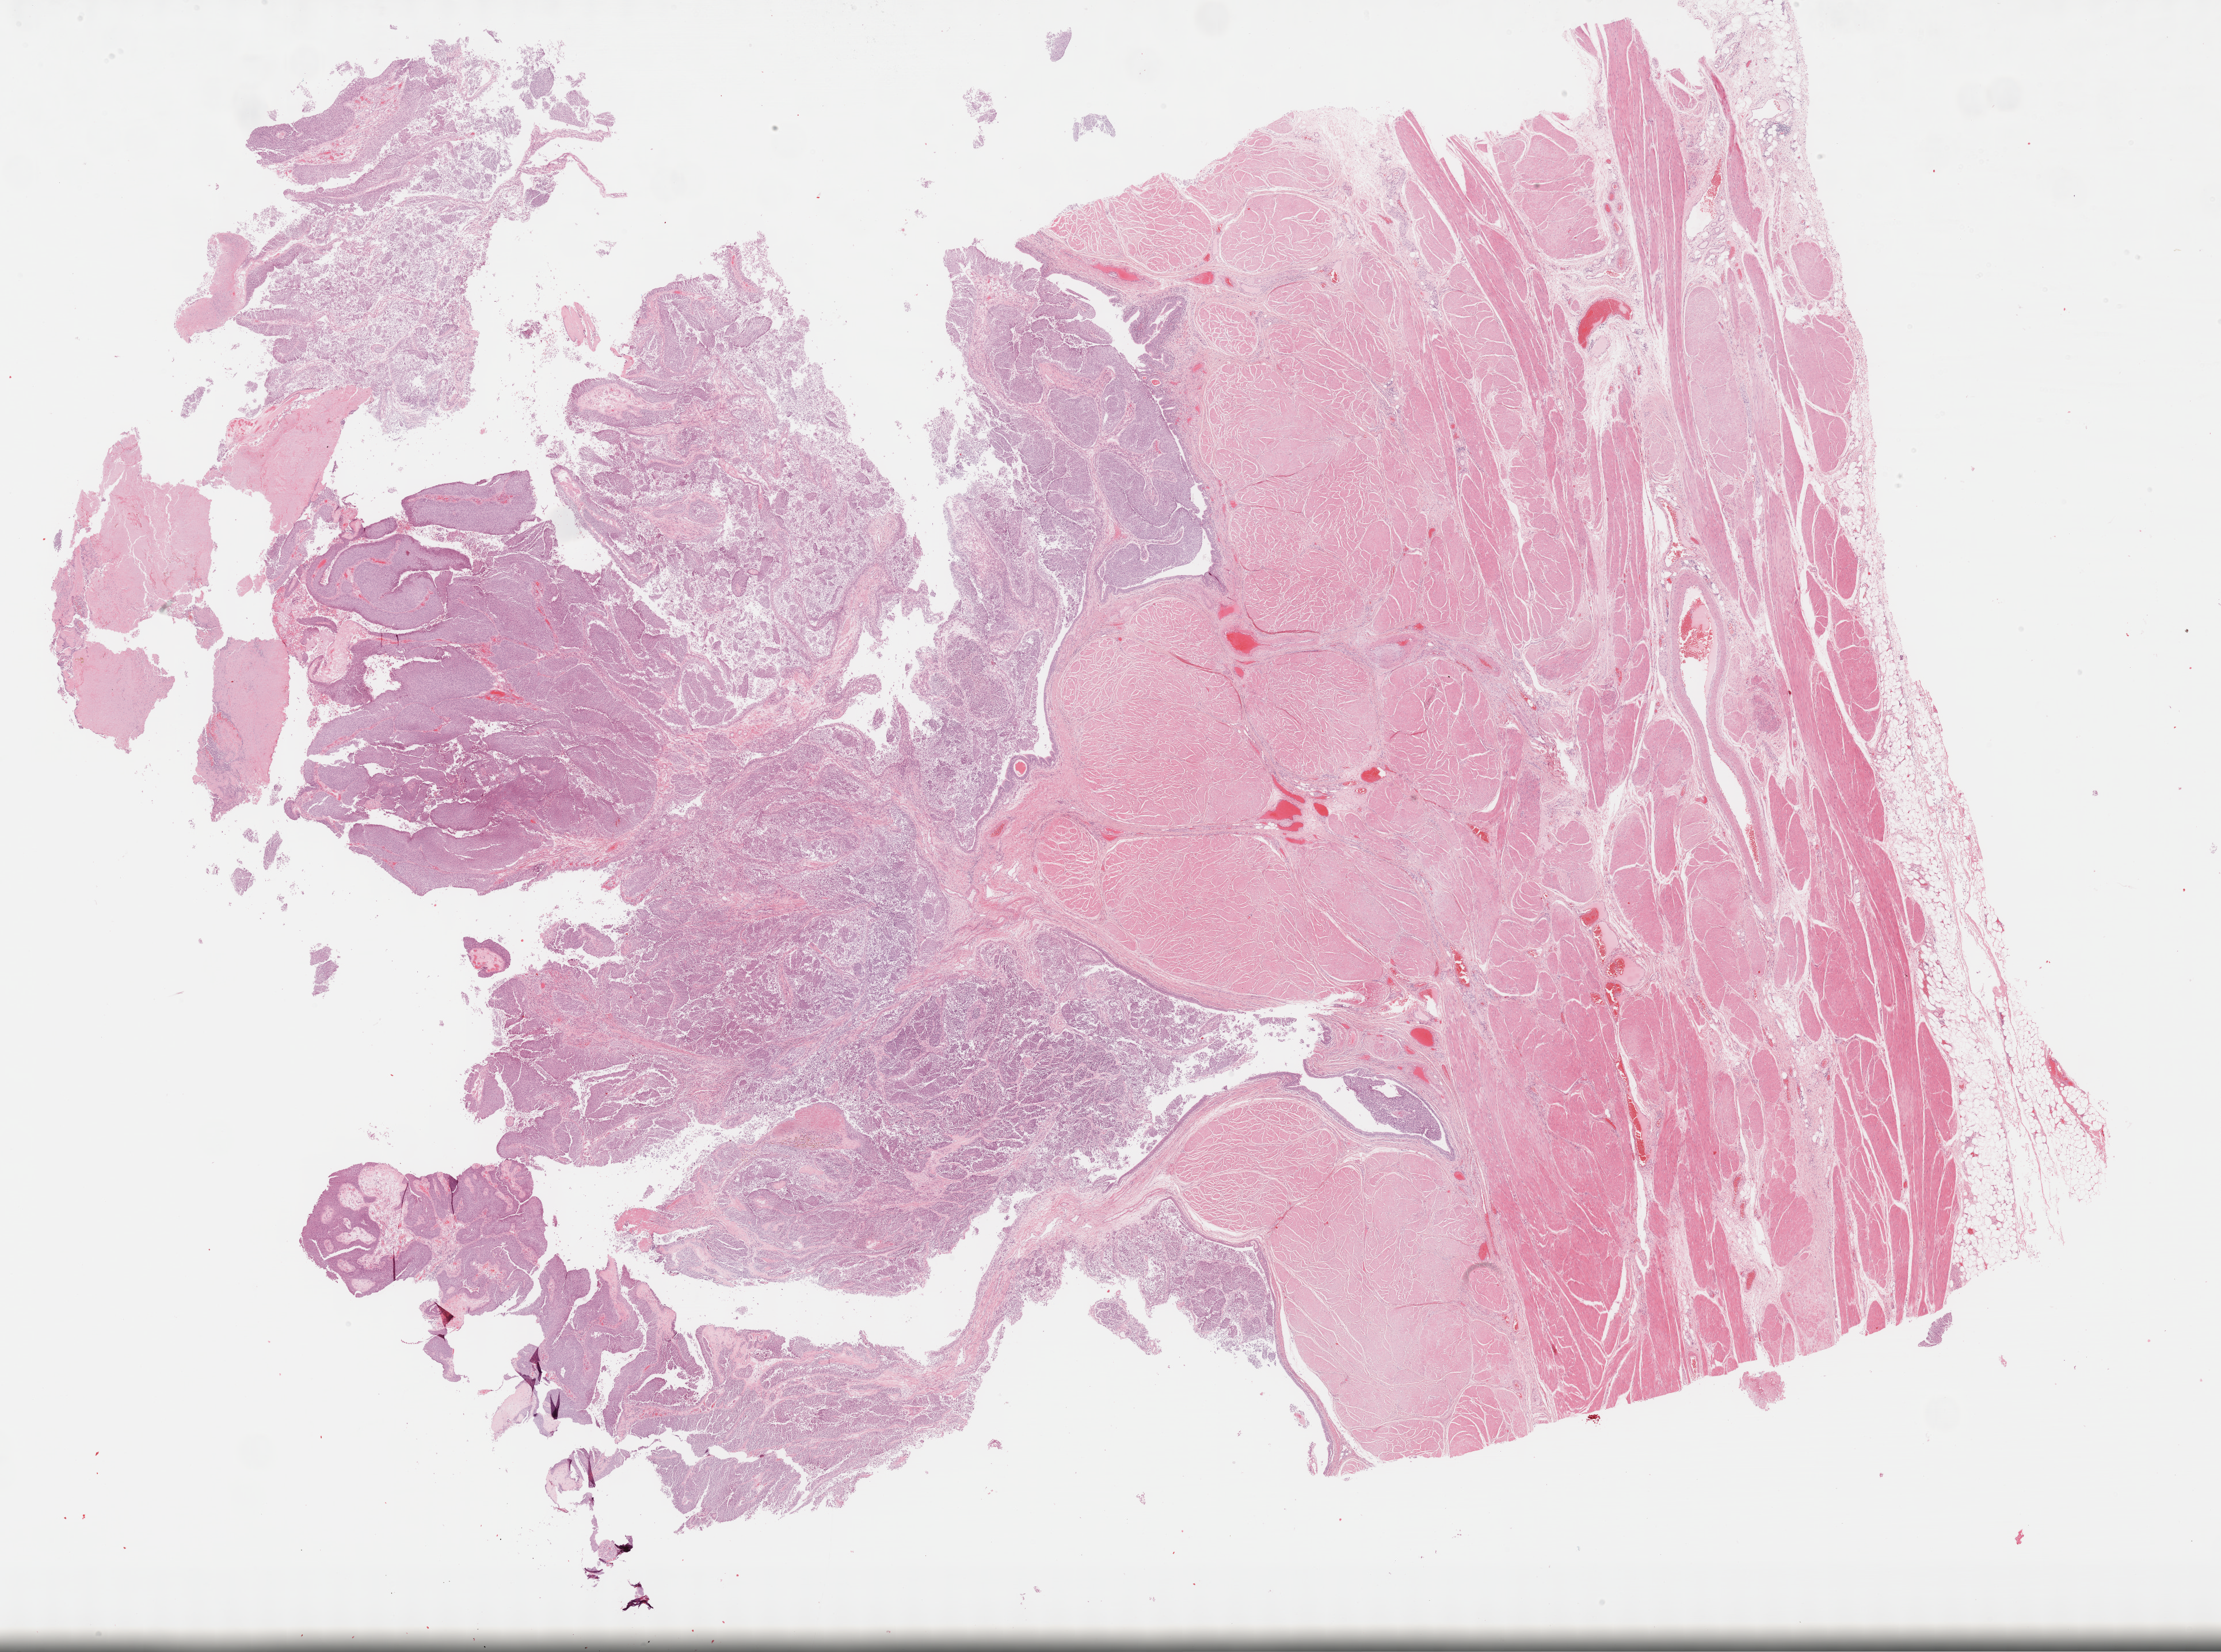
Digitized H&E-stained tissue section (whole slide), low-resolution overview of the scanned area, about 31.2 x 23.2 mm. Formalin-fixed paraffin-embedded (FFPE) diagnostic section. Bladder, primary tumour sample. Male, age 75 years at initial diagnosis.
Diagnosis: Papillary transitional cell carcinoma.